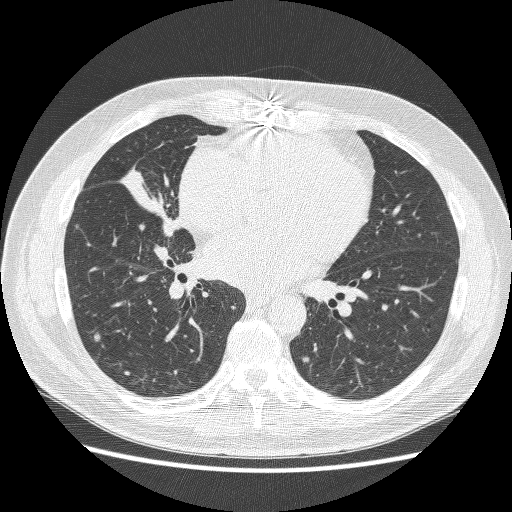
Axial slice from a low-dose chest CT screening exam; first (baseline) screen; lung window (W 1500 / L -600 HU); 120 kVp; slice 123 of 251 in the series. Male participant, aged 59 years at enrolment. Former smoker at enrolment.
Expert-annotated lung lesion, bounding box (x1, y1, x2, y2) in pixels: (110, 158, 196, 245). No non-calcified nodule or mass ≥4 mm was recorded by the screening reader at this exam. Official screen result: positive, change unspecified: nodule(s) >= 4 mm or enlarging nodule(s), mass(es), or other non-specific abnormalities suspicious for lung cancer. Later outcome: lung cancer diagnosed 24 days after this screen — adenocarcinoma, NOS, right middle lobe, poorly differentiated (G3), stage IV (AJCC 6th edition), 54 mm at pathology.